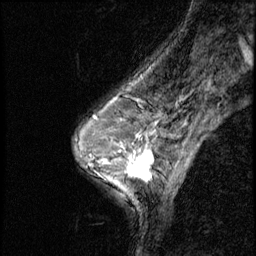
Breast MRI (dynamic contrast-enhanced), one sagittal slice; position 36 of 56 along the scan axis; dynamic contrast-enhanced series, image 2 of 3 at this slice position (ordered by acquisition); 1.5 T; TE 4.2 ms, TR 8.7 ms; 256 × 256 image matrix. Patient: female, 50 years. Case-level facts recorded for this patient, not image findings: setting: breast cancer imaged before/during neoadjuvant chemotherapy; receptor status: HR-positive, HER2-negative.
Structures marked on this image (semi-automatic segmentation, software-assisted and operator-edited):
- analysis volume of interest (the breast-tissue region the enhancement analysis was run in; not a lesion): bounding box (x1, y1, x2, y2) in pixels: (119, 136, 169, 190)
- tumour enhancement mask (voxels above the 140 % enhancement threshold inside the analysis volume of interest): (127, 149, 153, 180)